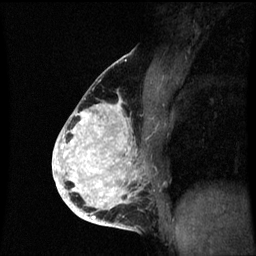
Breast MRI (dynamic contrast-enhanced), one sagittal slice; slice 36 of 60 in the series (ordered by position); dynamic contrast-enhanced series, image 2 of 3 at this slice position (ordered by acquisition); 1.5 T; TE 4.2 ms, TR 8.9 ms; 2 mm slice thickness; 256 × 256 image matrix, field of view 200 × 200 mm. Patient: female, 35 years. Case-level facts recorded for this patient, not image findings: setting: breast cancer imaged before/during neoadjuvant chemotherapy; receptor status: HR-positive, HER2-negative.
Annotated regions visible in this slice (semi-automatically segmented with operator editing):
- analysis volume of interest (the breast-tissue region the enhancement analysis was run in; not a lesion): bounding box <66,98,153,215> (left, top, right, bottom; pixels)
- tumour enhancement mask (voxels above the 70 % enhancement threshold inside the analysis volume of interest): <66,104,131,215>